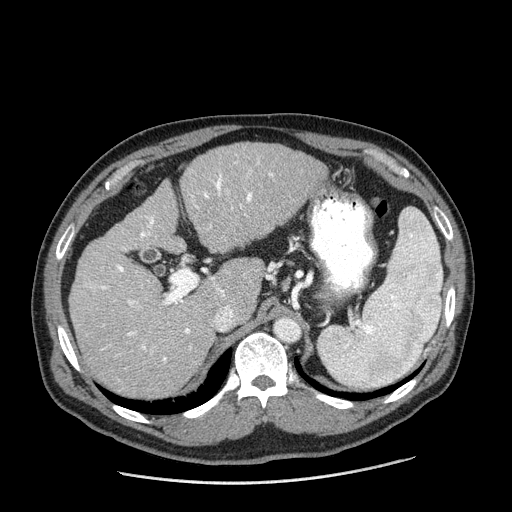
Contrast-enhanced abdominal CT (liver protocol), one axial slice; position 121 of 198 along the scan axis; one of 2 acquisitions stored at this slice position; soft-tissue window (W 400 / L 40 HU); 2.5 mm slice thickness; 512 × 512 image matrix, field of view 400 × 400 mm. From the clinical record (not read from this slice): diagnosis: hepatocellular carcinoma (patient treated with transarterial chemoembolisation; whether this scan precedes or follows treatment is not stated here); TNM stage (as recorded): Stage-II; Child-Pugh class: A; tumour differentiation: moderately differentiated; tumour nodularity: multinodular.
Outlined on this slice (semi-automatically segmented with operator editing):
- liver parenchyma outside the tumour (the mass and vessels are separate outlines, so this box may not span the whole liver): bounding box (x1, y1, x2, y2) in pixels: (68, 142, 328, 398)
- liver vessels: (100, 161, 273, 361)